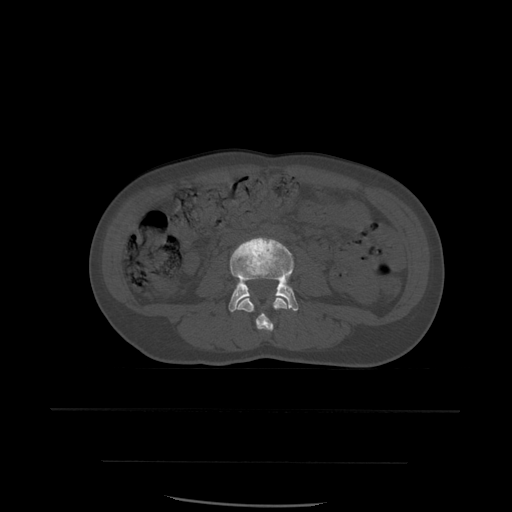
CT including the spine, one axial slice. Position 182 of 574 along the scan axis. Bone window (W 1800 / L 400 HU). 1.25 mm slice thickness. 512 × 512 image matrix, field of view 392 × 392 mm. Patient age 48 years. From the clinical record (not read from this slice): primary cancer: lung.
Structures marked on this image (semi-automatically segmented with operator editing):
- L3 vertebra: bounding box (x1, y1, x2, y2) in pixels: (236, 298, 289, 332)
- L4 vertebra: (229, 237, 299, 312)